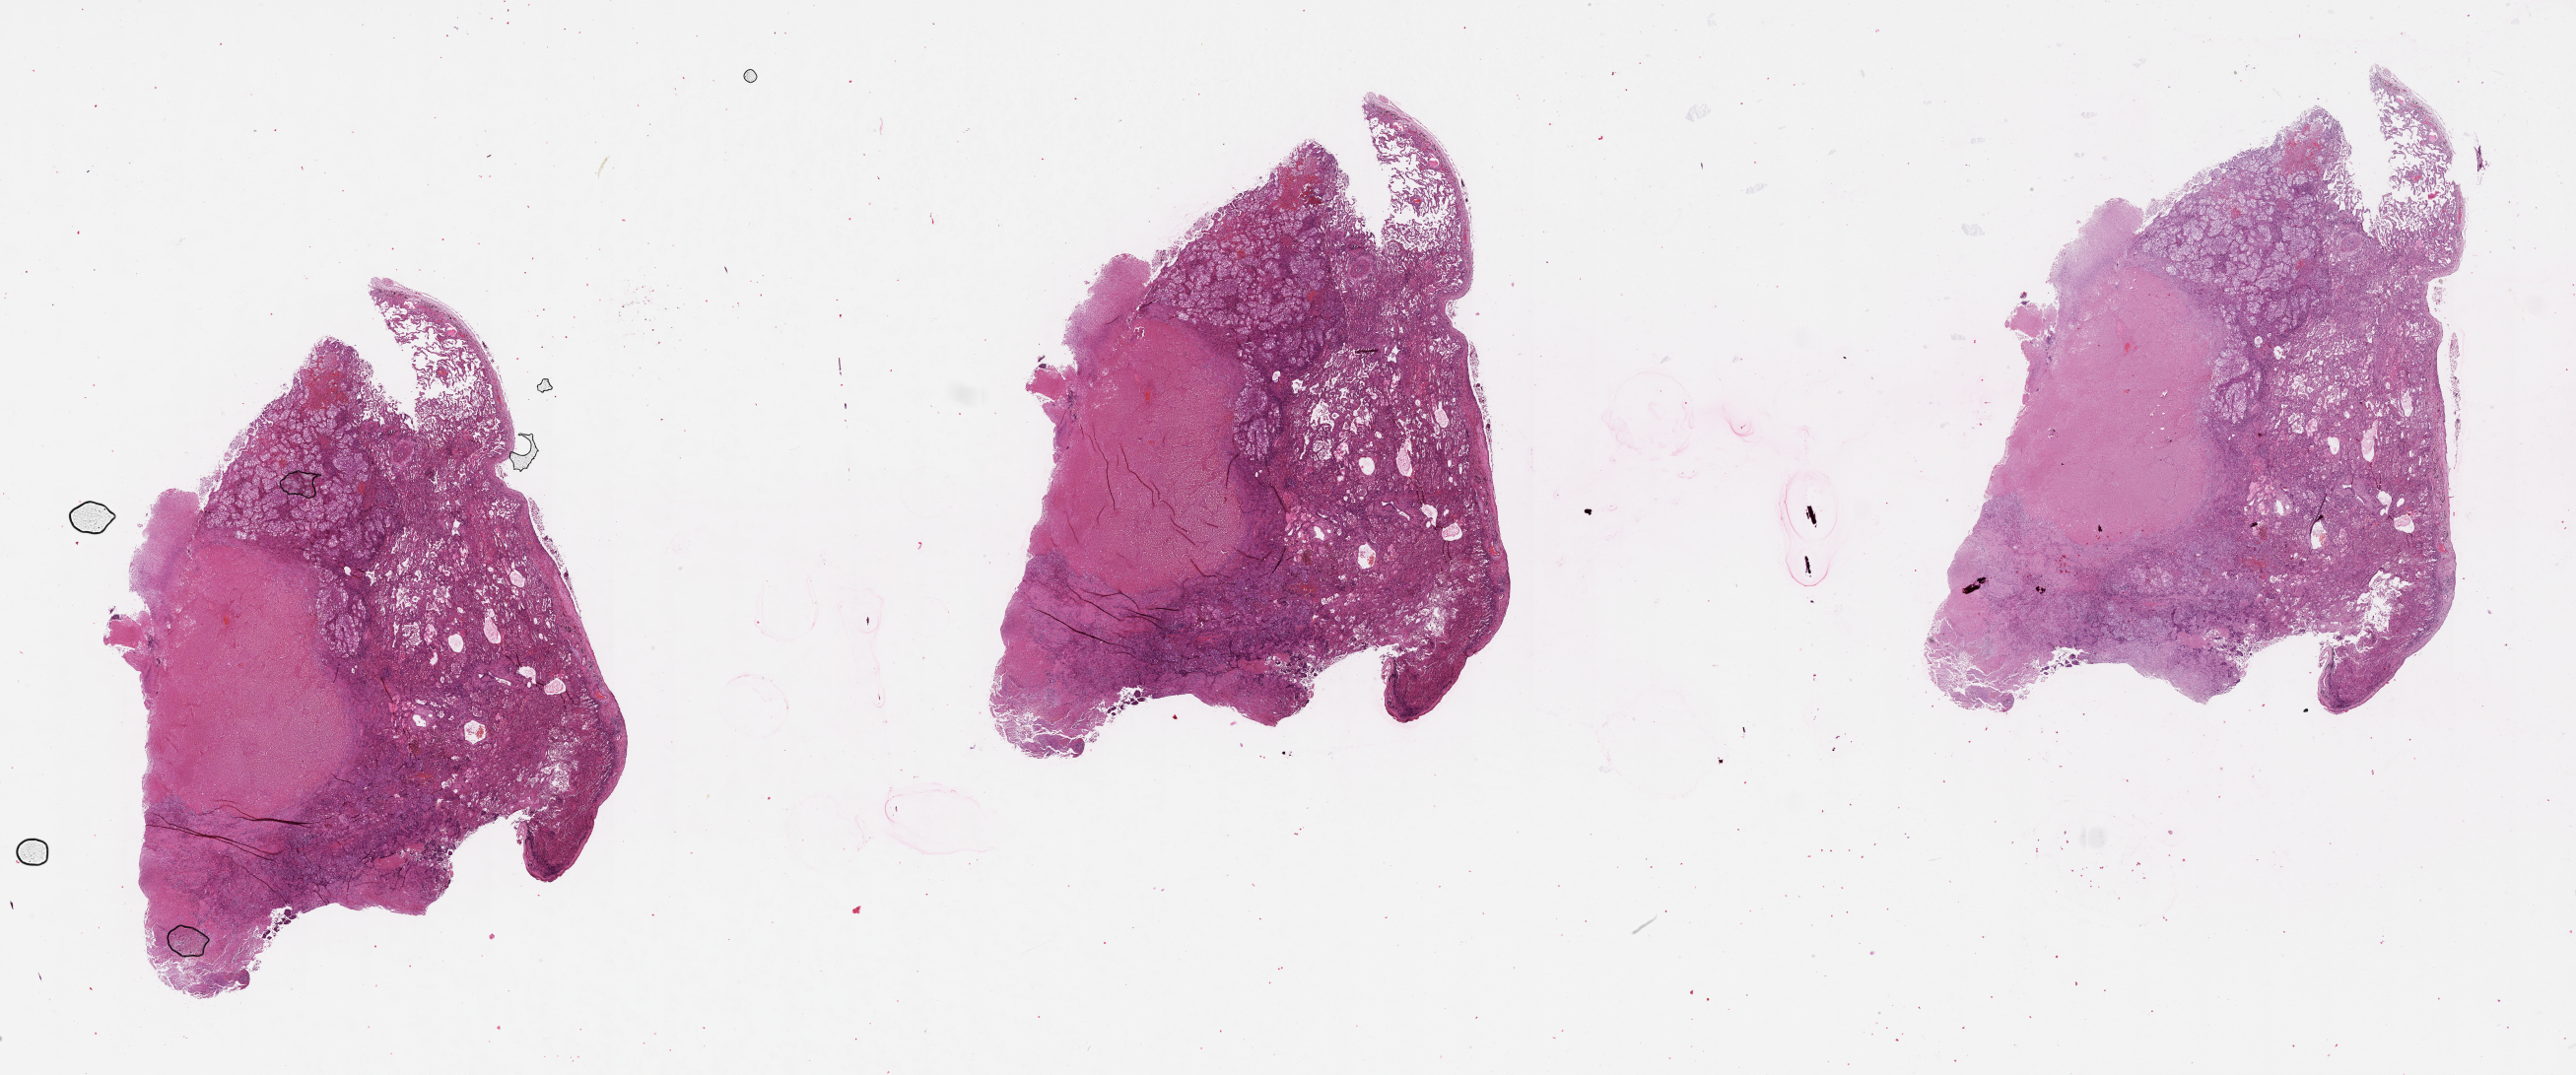
Whole-slide histology image, H&E, a low-resolution overview of the entire scanned area, about 42.1 x 17.6 mm; lung, tissue type not recorded.
• patient diagnosis (cohort enrolment): lung adenocarcinoma (lung)